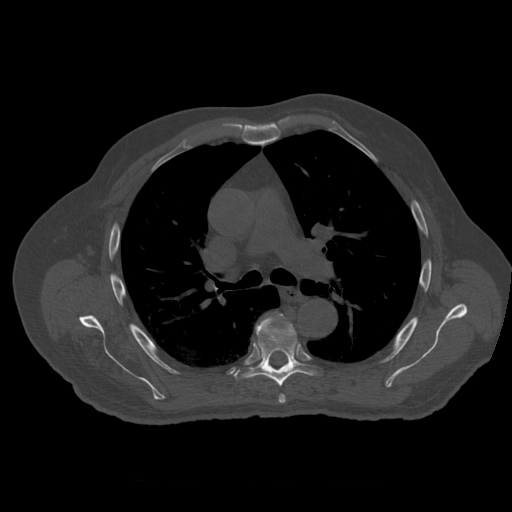
CT including the spine, one axial slice. Position 385 of 399 along the scan axis. 120 kVp. Bone window (W 1800 / L 400 HU). 1.25 mm slice thickness. 512 × 512 image matrix, field of view 407 × 407 mm. Patient age 73 years. Case-level facts recorded for this patient, not image findings: primary cancer: prostate.
Outlined on this slice (semi-automatically segmented with operator editing):
- T5 vertebra: bounding box (x1, y1, x2, y2) in pixels: (279, 395, 286, 404)
- T6 vertebra: (235, 316, 324, 387)